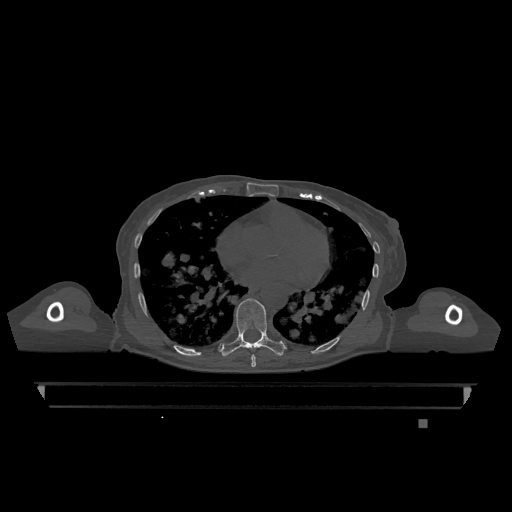
CT including the spine, one axial slice. Position 697 of 1317 along the scan axis. Bone window (W 1800 / L 400 HU). 0.5 mm slice thickness. 512 × 512 image matrix, field of view 500 × 500 mm. Patient: female, 74 years. From the clinical record (not read from this slice): primary cancer: lung.
Outlined on this slice (semi-automatic segmentation, software-assisted and operator-edited):
- T7 vertebra: box from (x=251, y=355) to (x=256, y=367) px
- T9 vertebra: (x=222, y=298)–(x=284, y=357)